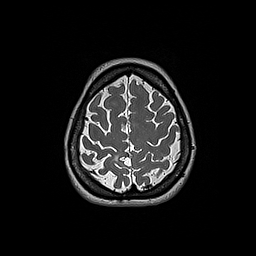
Brain MRI from a brain-tumour surgery series, one axial slice. Position 49 of 192 along the scan axis. 1 mm slice thickness. 256 × 256 image matrix. From the clinical record (not read from this slice): histopathology: Oligodendroglioma; WHO grade: 2; IDH mutation: yes; tumour location: Right Parietal.
Annotated regions visible in this slice (expert manual segmentation):
- tumour: box from (x=114, y=155) to (x=118, y=161) px